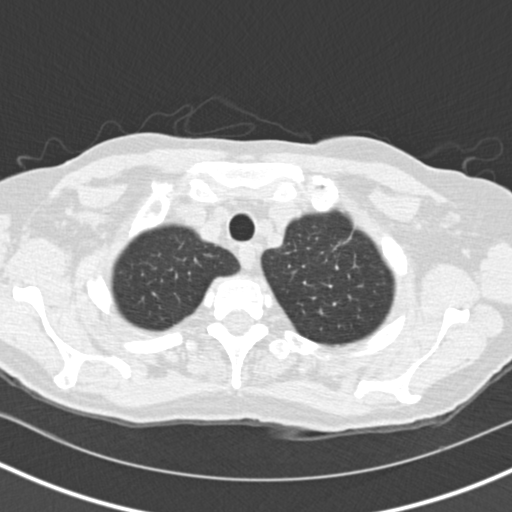
Chest CT (low-dose screening protocol), one axial image. Baseline annual screen. Lung window (W 1500 / L -600 HU). Standard (soft-tissue) reconstruction kernel (B30f). 512 × 512 image matrix, field of view 310 × 310 mm. Female participant, aged 73 years at enrolment.
Lesion marked by an expert reader, bounding box (x1, y1, x2, y2) in pixels: (306, 234, 357, 292). Reader record for this screening exam (exam-level; its link to the box is not recorded): non-calcified nodule or mass ≥4 mm, left upper lobe, 27 × 21 mm, spiculated (stellate) margins, soft tissue attenuation. Lung cancer was diagnosed 72 days after this screen: bronchiolo-alveolar adenocarcinoma, NOS, left upper lobe, moderately differentiated (G2), stage IIIB (AJCC 6th edition), 17 mm at pathology.